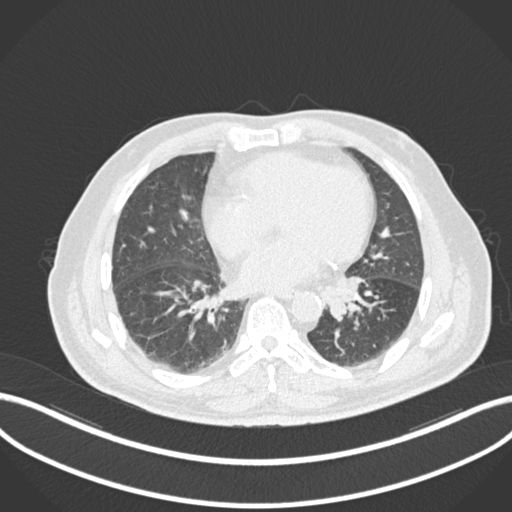
Chest CT, one axial slice; slice 45 of 161 in the series (ordered by position); lung window (W 1500 / L -600 HU); 1 mm slice thickness; 512 × 512 image matrix. Patient: male, 71 years. From the clinical record (not read from this slice): clinical TNM (as recorded): T1b N0 M0.
Outlined on this slice (bounding box drawn by a radiologist):
- lung tumour (recorded histology: squamous cell carcinoma): box from (x=322, y=276) to (x=366, y=326) px